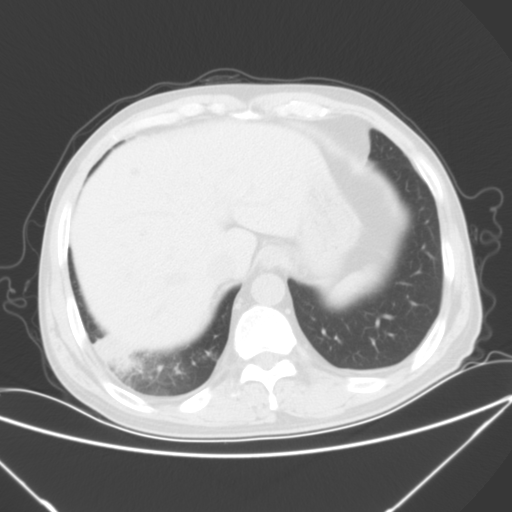
Chest CT, one axial slice. Position 14 of 57 along the scan axis. 120 kVp. Lung window (W 1500 / L -600 HU). 5 mm slice thickness. 512 × 512 image matrix, field of view 364 × 364 mm. Male patient, age 54 years. From the clinical record (not read from this slice): clinical TNM (as recorded): T2 N1 M0.
Annotated regions visible in this slice (rectangle marked by the reading radiologist):
- lung tumour (recorded histology: adenocarcinoma): box from (x=90, y=327) to (x=133, y=370) px